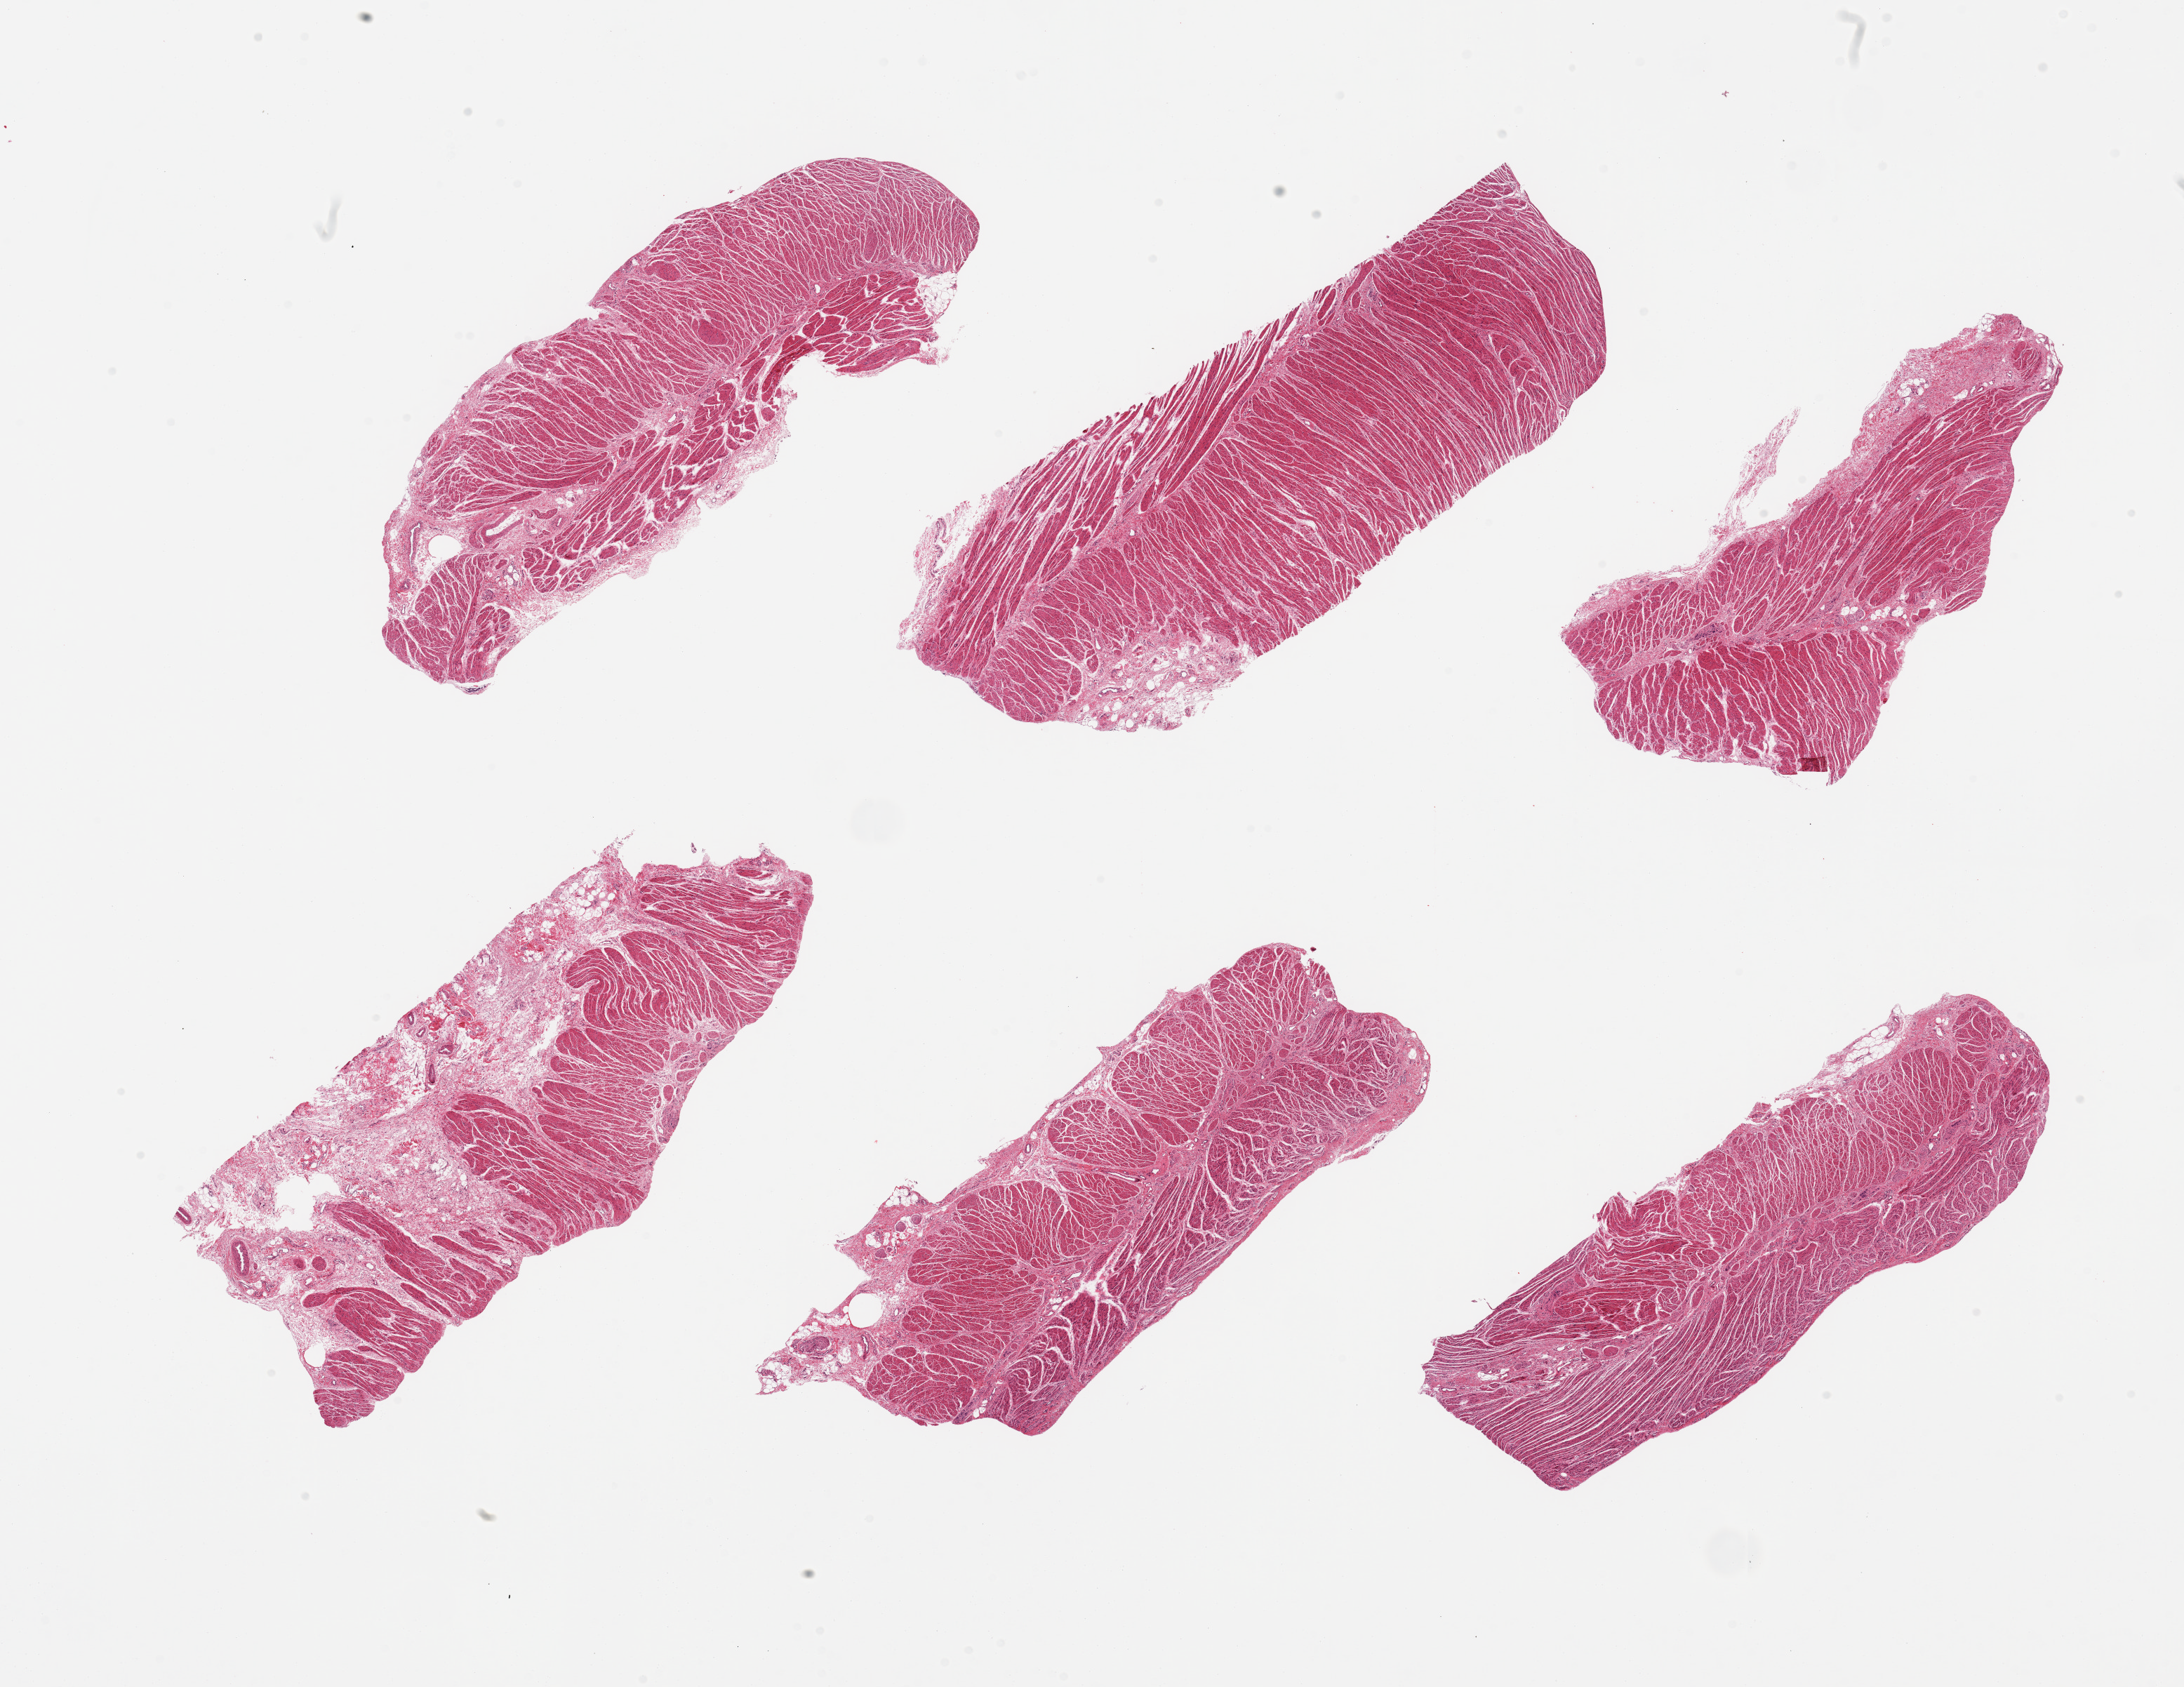
Whole-slide image, H&E stain — shown as a low-resolution overview of the whole scanned area (about 24.6 x 19.0 mm, from a 20x scan). PAXgene-fixed, paraffin-embedded tissue. Sampled site (target tissue): gastroesophageal junction. Donor tissue sample. Female donor.
Review note (as recorded): 6 pieces; predominantly well trimmed.